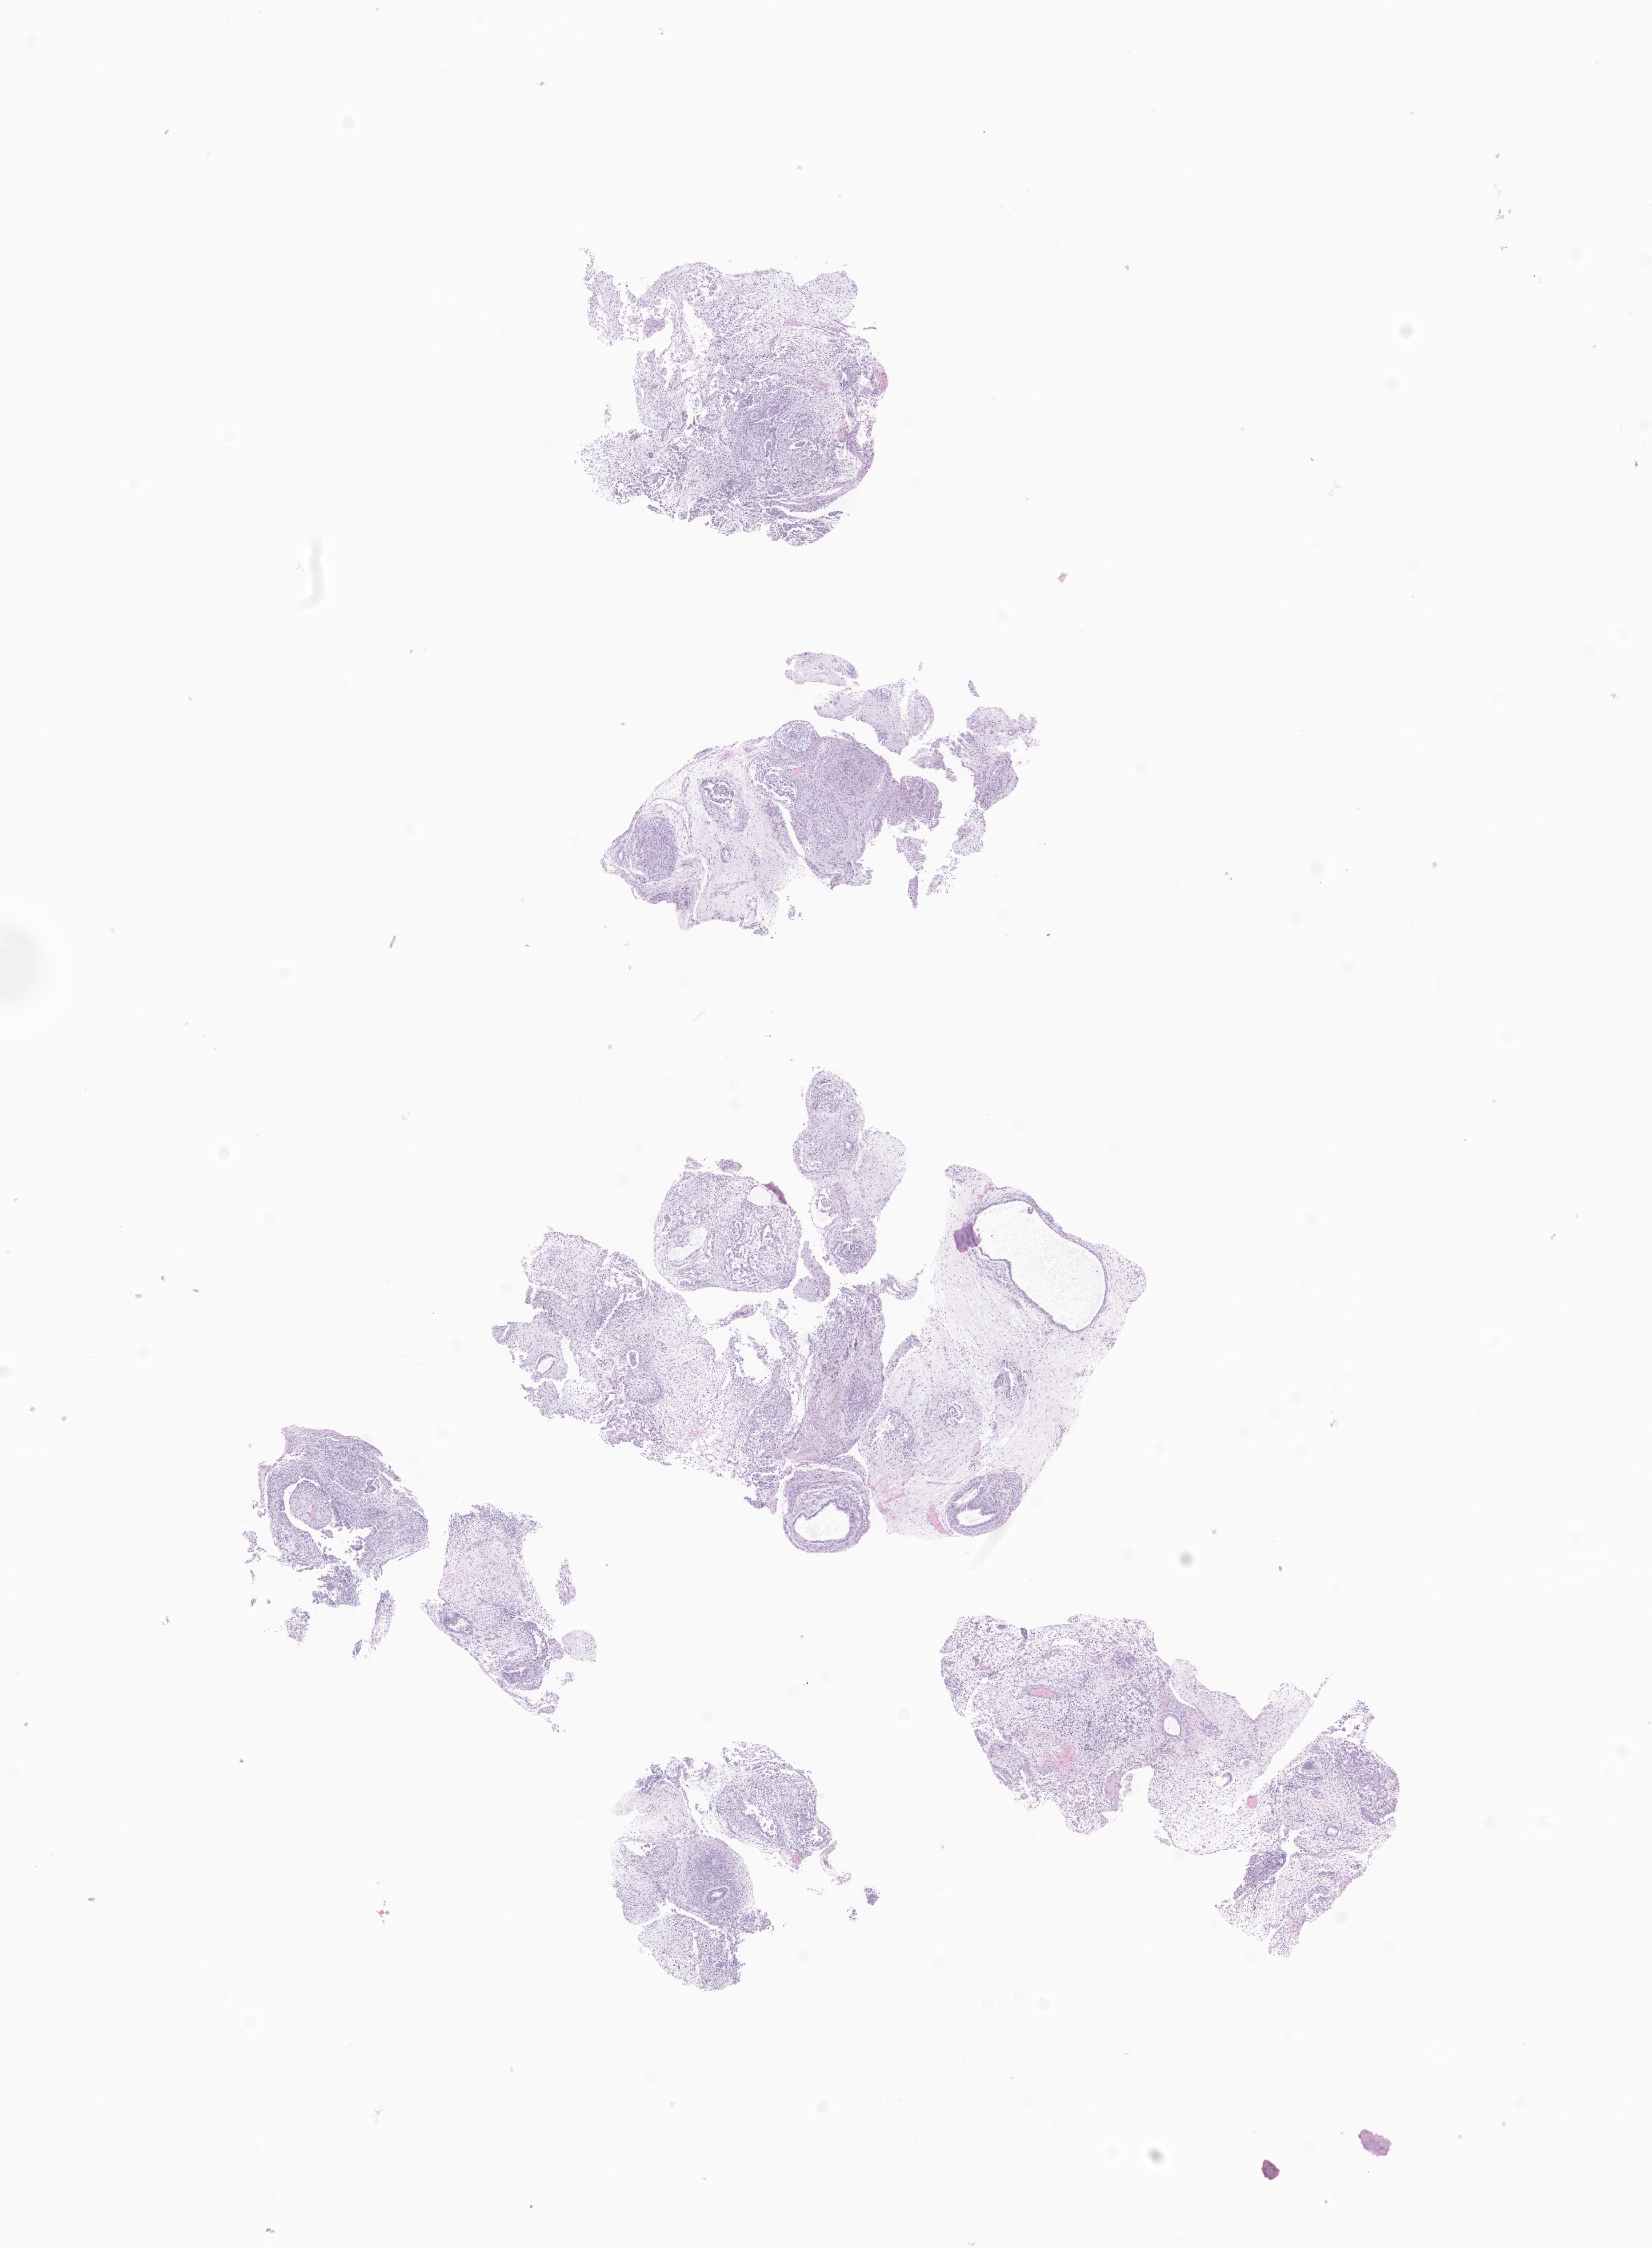
Hematoxylin and eosin (H&E) whole-slide image of tumor tissue from the brain — whole scanned area (about 12.2 x 16.6 mm) shown as a low-resolution overview; formalin-fixed paraffin-embedded section. Male patient, age 117 months (9 years 9 months).
Recorded diagnosis: Neoplasm, malignant.